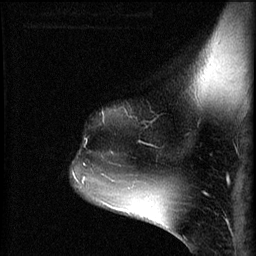
Breast MRI (dynamic contrast-enhanced), one sagittal slice; slice 47 of 60 in the series (ordered by position); 3 images stored at this slice position (order not interpretable as contrast timing); 1.5 T; TE 4.2 ms, TR 8.2 ms; 2 mm slice thickness; 256 × 256 image matrix, field of view 180 × 180 mm. Patient: female, 49 years.
Annotated regions visible in this slice (semi-automatically segmented with operator editing):
- analysis volume of interest (the breast-tissue region the enhancement analysis was run in; not a lesion): bounding box [x1, y1, x2, y2] px = [73, 162, 109, 187]
- tumour enhancement mask (voxels above the 70 % enhancement threshold inside the analysis volume of interest): [83, 178, 85, 181]